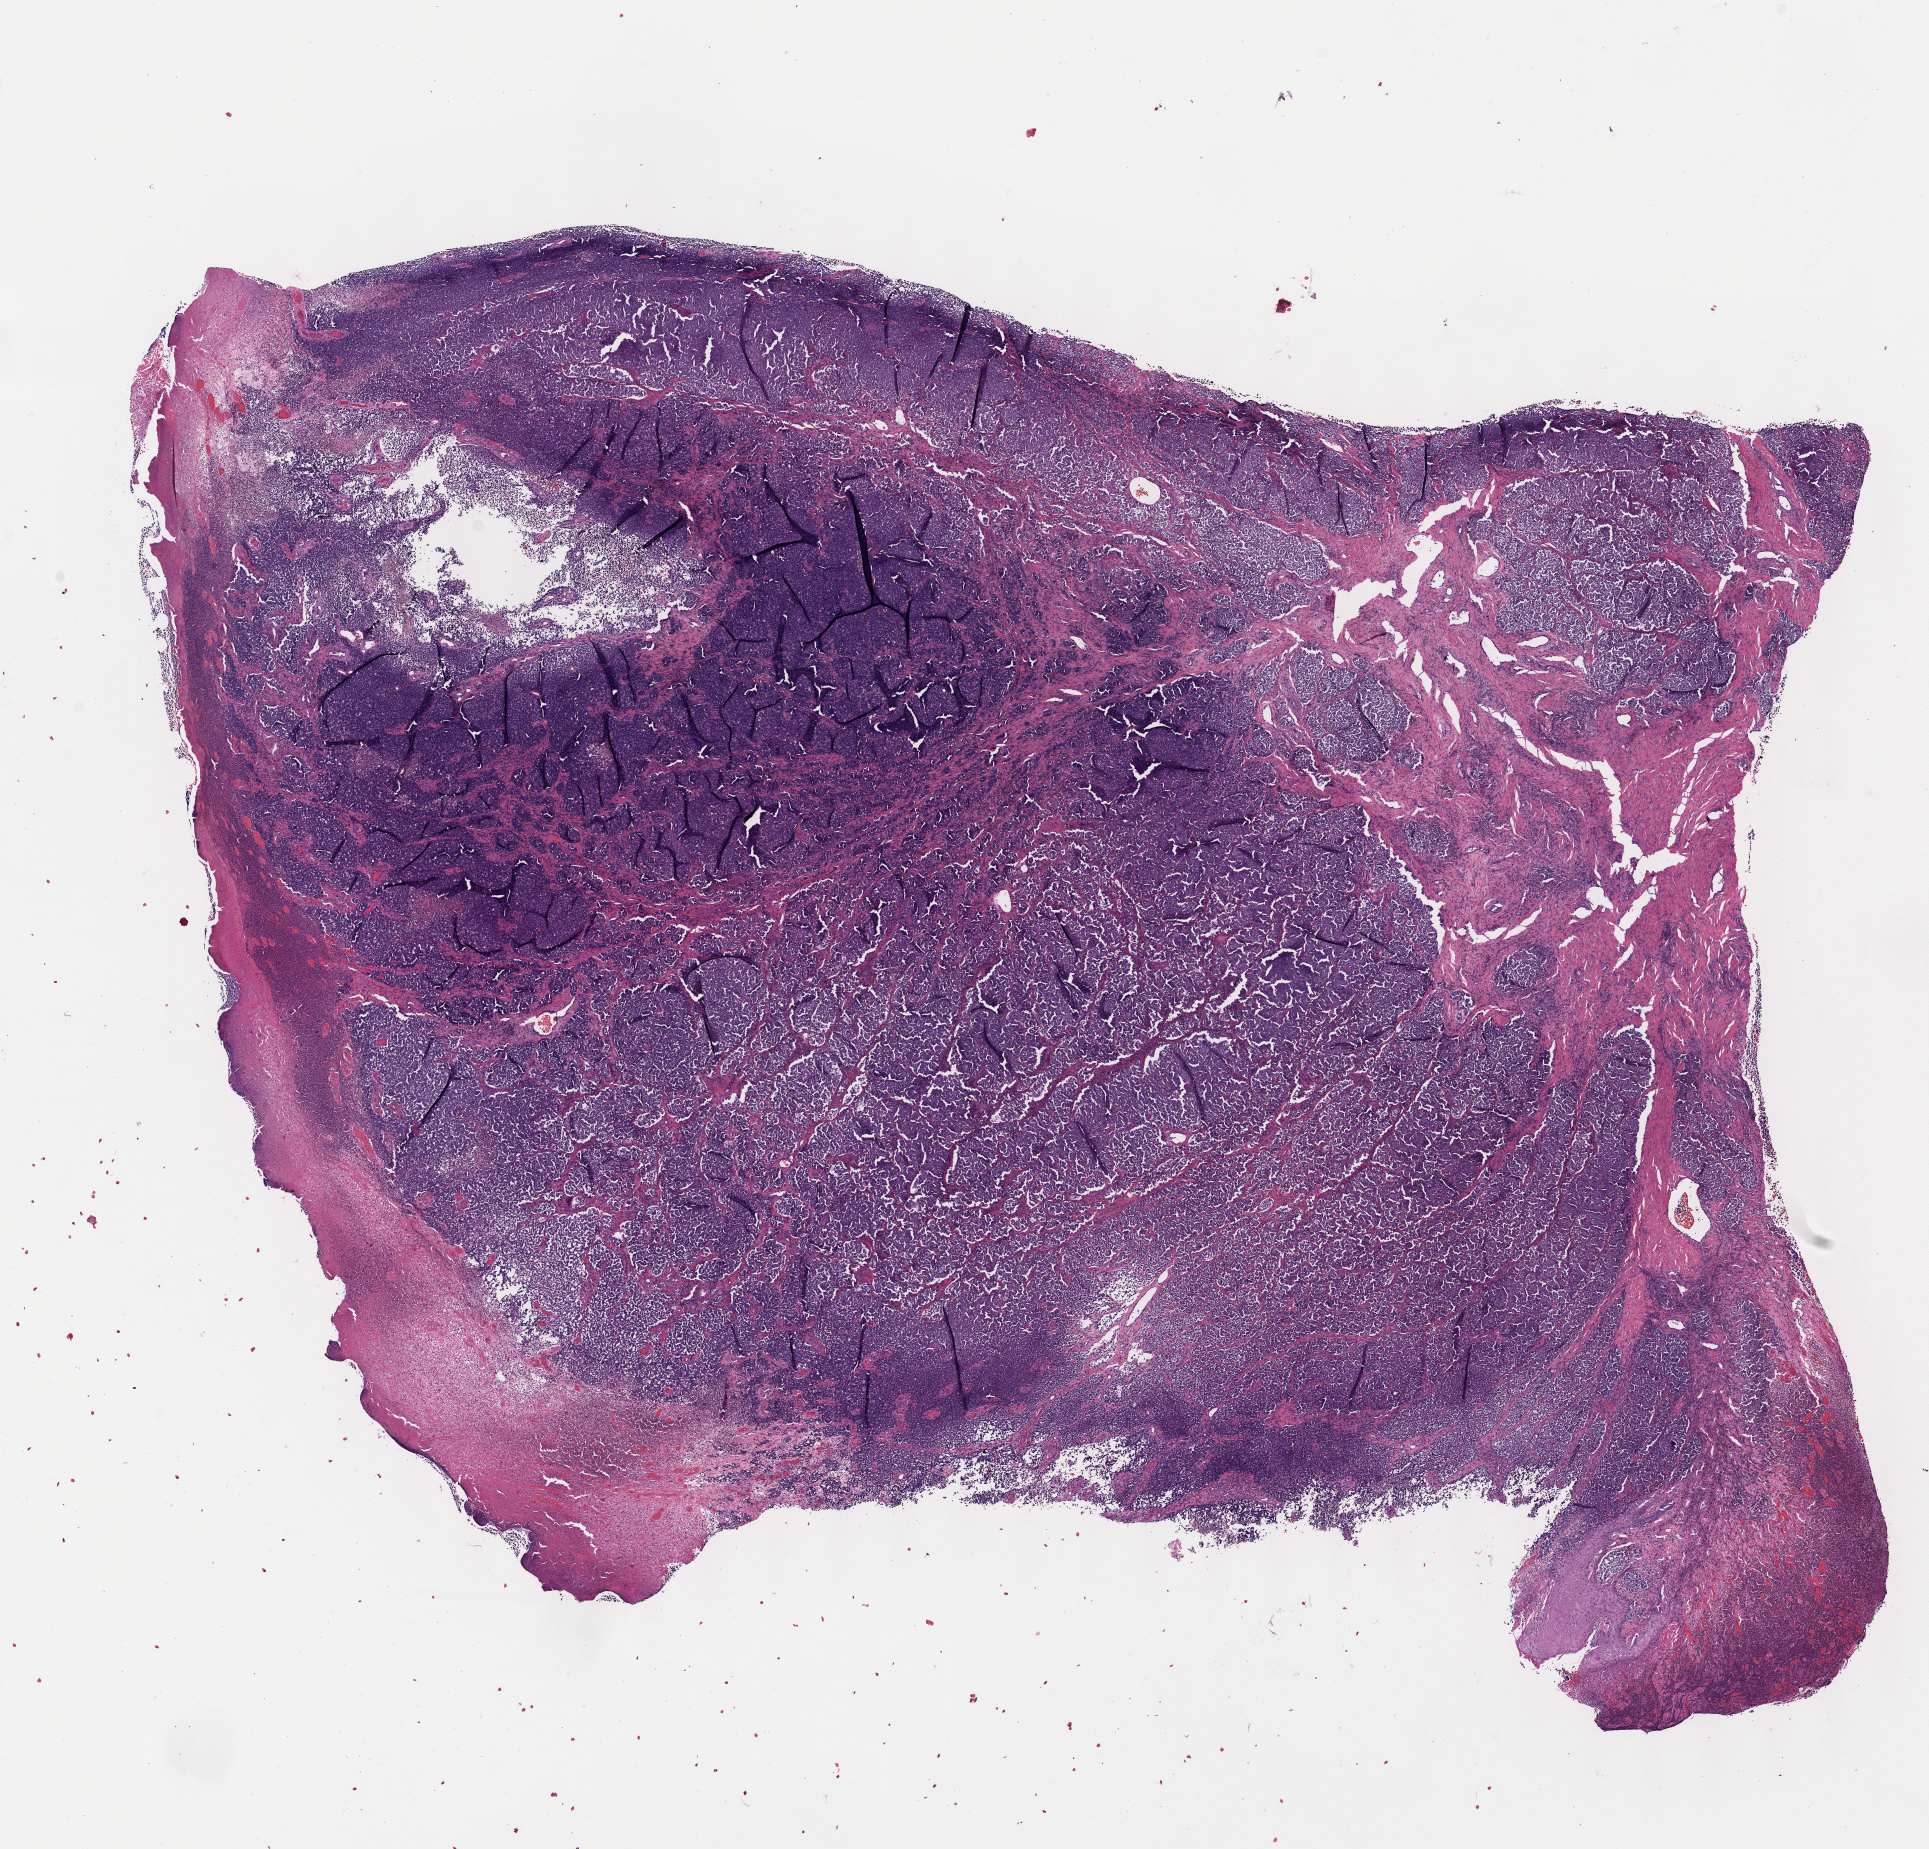
Digitized H&E tissue section (whole slide) — low-resolution overview of the scanned area, about 15.6 x 14.9 mm, formalin-fixed paraffin-embedded (FFPE) diagnostic section, skin, primary tumour sample. Male patient; age at initial diagnosis 55 years.
* histologic diagnosis: Epithelioid cell melanoma
* AJCC pathologic stage: III (7th edition)